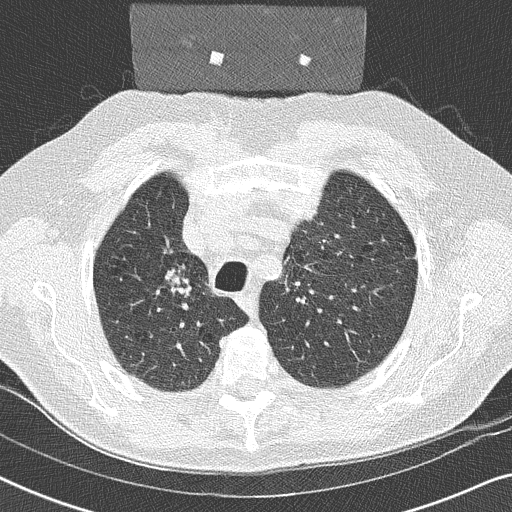
Chest CT (low-dose screening protocol), one axial image, second annual screen, lung window (W 1500 / L -600 HU), 2 mm slice thickness, lung (sharp) reconstruction kernel (B50f), 120 kVp, slice 67 of 252 in the series, 512 × 512 image matrix, field of view 330 × 330 mm. Male participant, aged 59 years at enrolment.
• Lesion marked by an expert reader, box from (x=155, y=261) to (x=209, y=308) px.
• Reader record for this screening exam (exam-level; its link to the box is not recorded): non-calcified nodule or mass ≥4 mm, right upper lobe, 17 × 16 mm, smooth margins, soft tissue attenuation, pre-existing on the prior screen: yes.
• Lung cancer was diagnosed 14 days after this screen: squamous cell carcinoma, NOS, right upper lobe, poorly differentiated (G3), stage IIA (AJCC 6th edition), 20 mm at pathology.